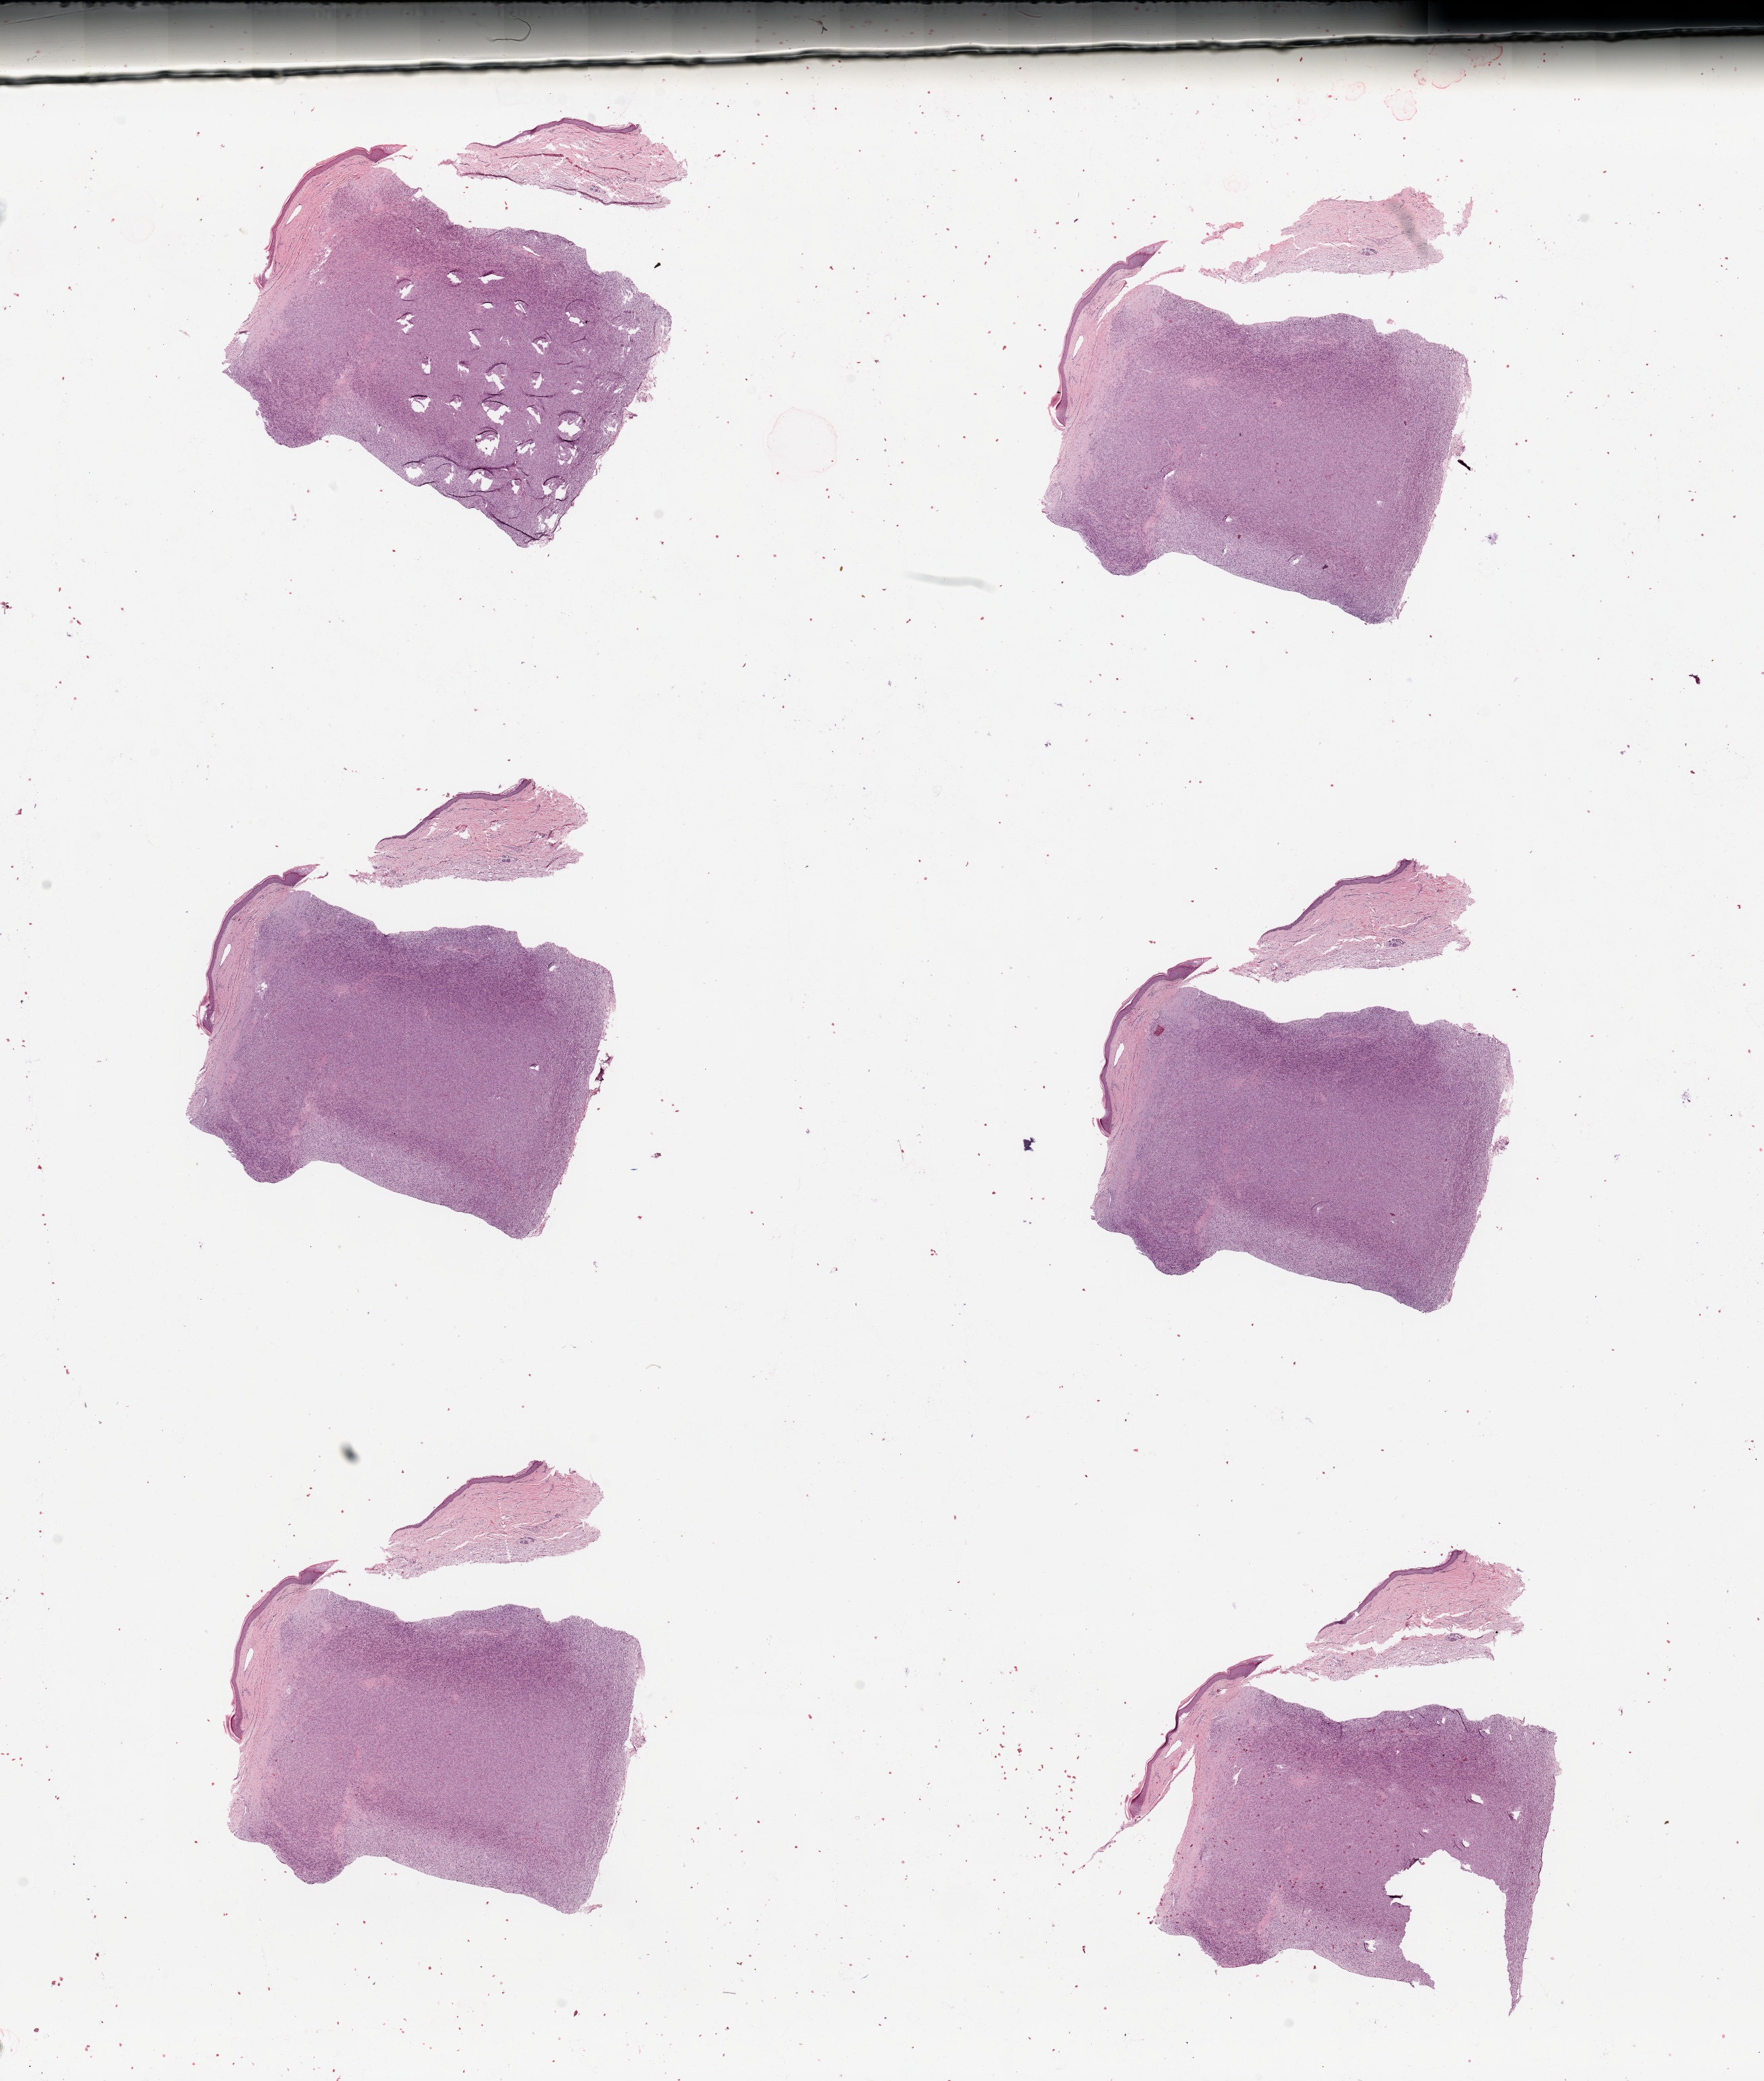
Digitized H&E tissue section (whole slide), whole scanned area (about 20.7 x 24.4 mm) shown as a low-resolution overview, tumour tissue sample. 68-year-old male patient.
- patient diagnosis (cohort enrolment): sarcoma (site not recorded at cohort level)